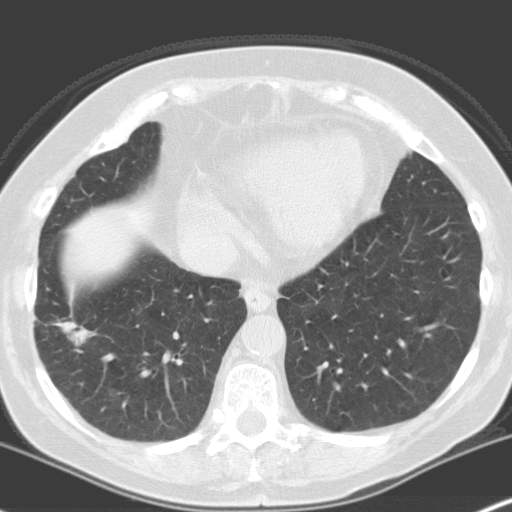
Low-dose screening chest CT, axial slice, baseline annual screen, lung window (W 1500 / L -600 HU), 3.2 mm slice thickness, slice 101 of 160 in the series, 512 × 512 image matrix, field of view 316 × 316 mm. Female, age 70 years at enrolment. Current smoker at enrolment.
Expert-annotated lung lesion, box from (x=29, y=293) to (x=101, y=363) px. The screening reader recorded 4 non-calcified nodules or masses ≥4 mm on this exam; which of them this box marks is not recorded. Official screen result: positive, change unspecified: nodule(s) >= 4 mm or enlarging nodule(s), mass(es), or other non-specific abnormalities suspicious for lung cancer. Later outcome: lung cancer diagnosed 28 days after this screen — adenocarcinoma, NOS, right lower lobe, moderately differentiated (G2), stage IV (AJCC 6th edition), 28 mm at pathology.